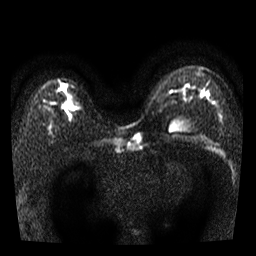
Breast MRI, one axial slice. Position 23 of 39 along the scan axis. Diffusion-weighted series; image 2 of 4 stored at this slice position (different b-values; order by instance number). 3 T. 5 mm slice thickness. 256 × 256 image matrix, field of view 280 × 280 mm. Female patient.
Structures marked on this image (outlined manually by an expert reader):
- tumour on diffusion-weighted imaging: box from (x=63, y=102) to (x=67, y=107) px